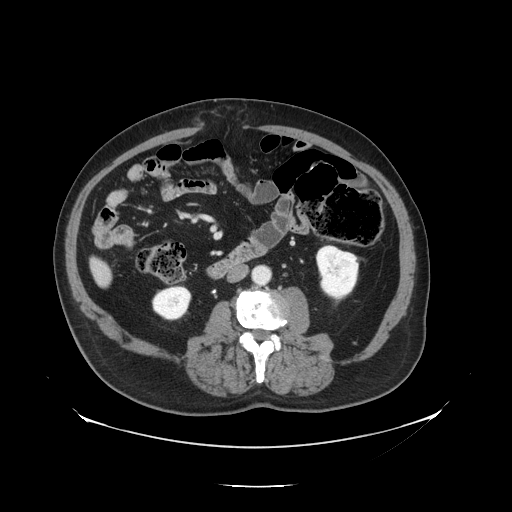
Contrast-enhanced abdominal CT, one axial slice; position 32 of 138 along the scan axis; reconstruction kernel STANDARD; soft-tissue window (W 400 / L 40 HU); 512 × 512 image matrix, field of view 497 × 497 mm. Male patient, age 77 years. From the clinical record (not read from this slice): diagnosis: colorectal cancer liver metastases, imaged before liver resection.
Structures marked on this image (outlined manually by an expert reader):
- liver: bounding box <92,261,111,285> (left, top, right, bottom; pixels)
- planned liver remnant (the part of the liver to remain after resection): <93,261,107,274>